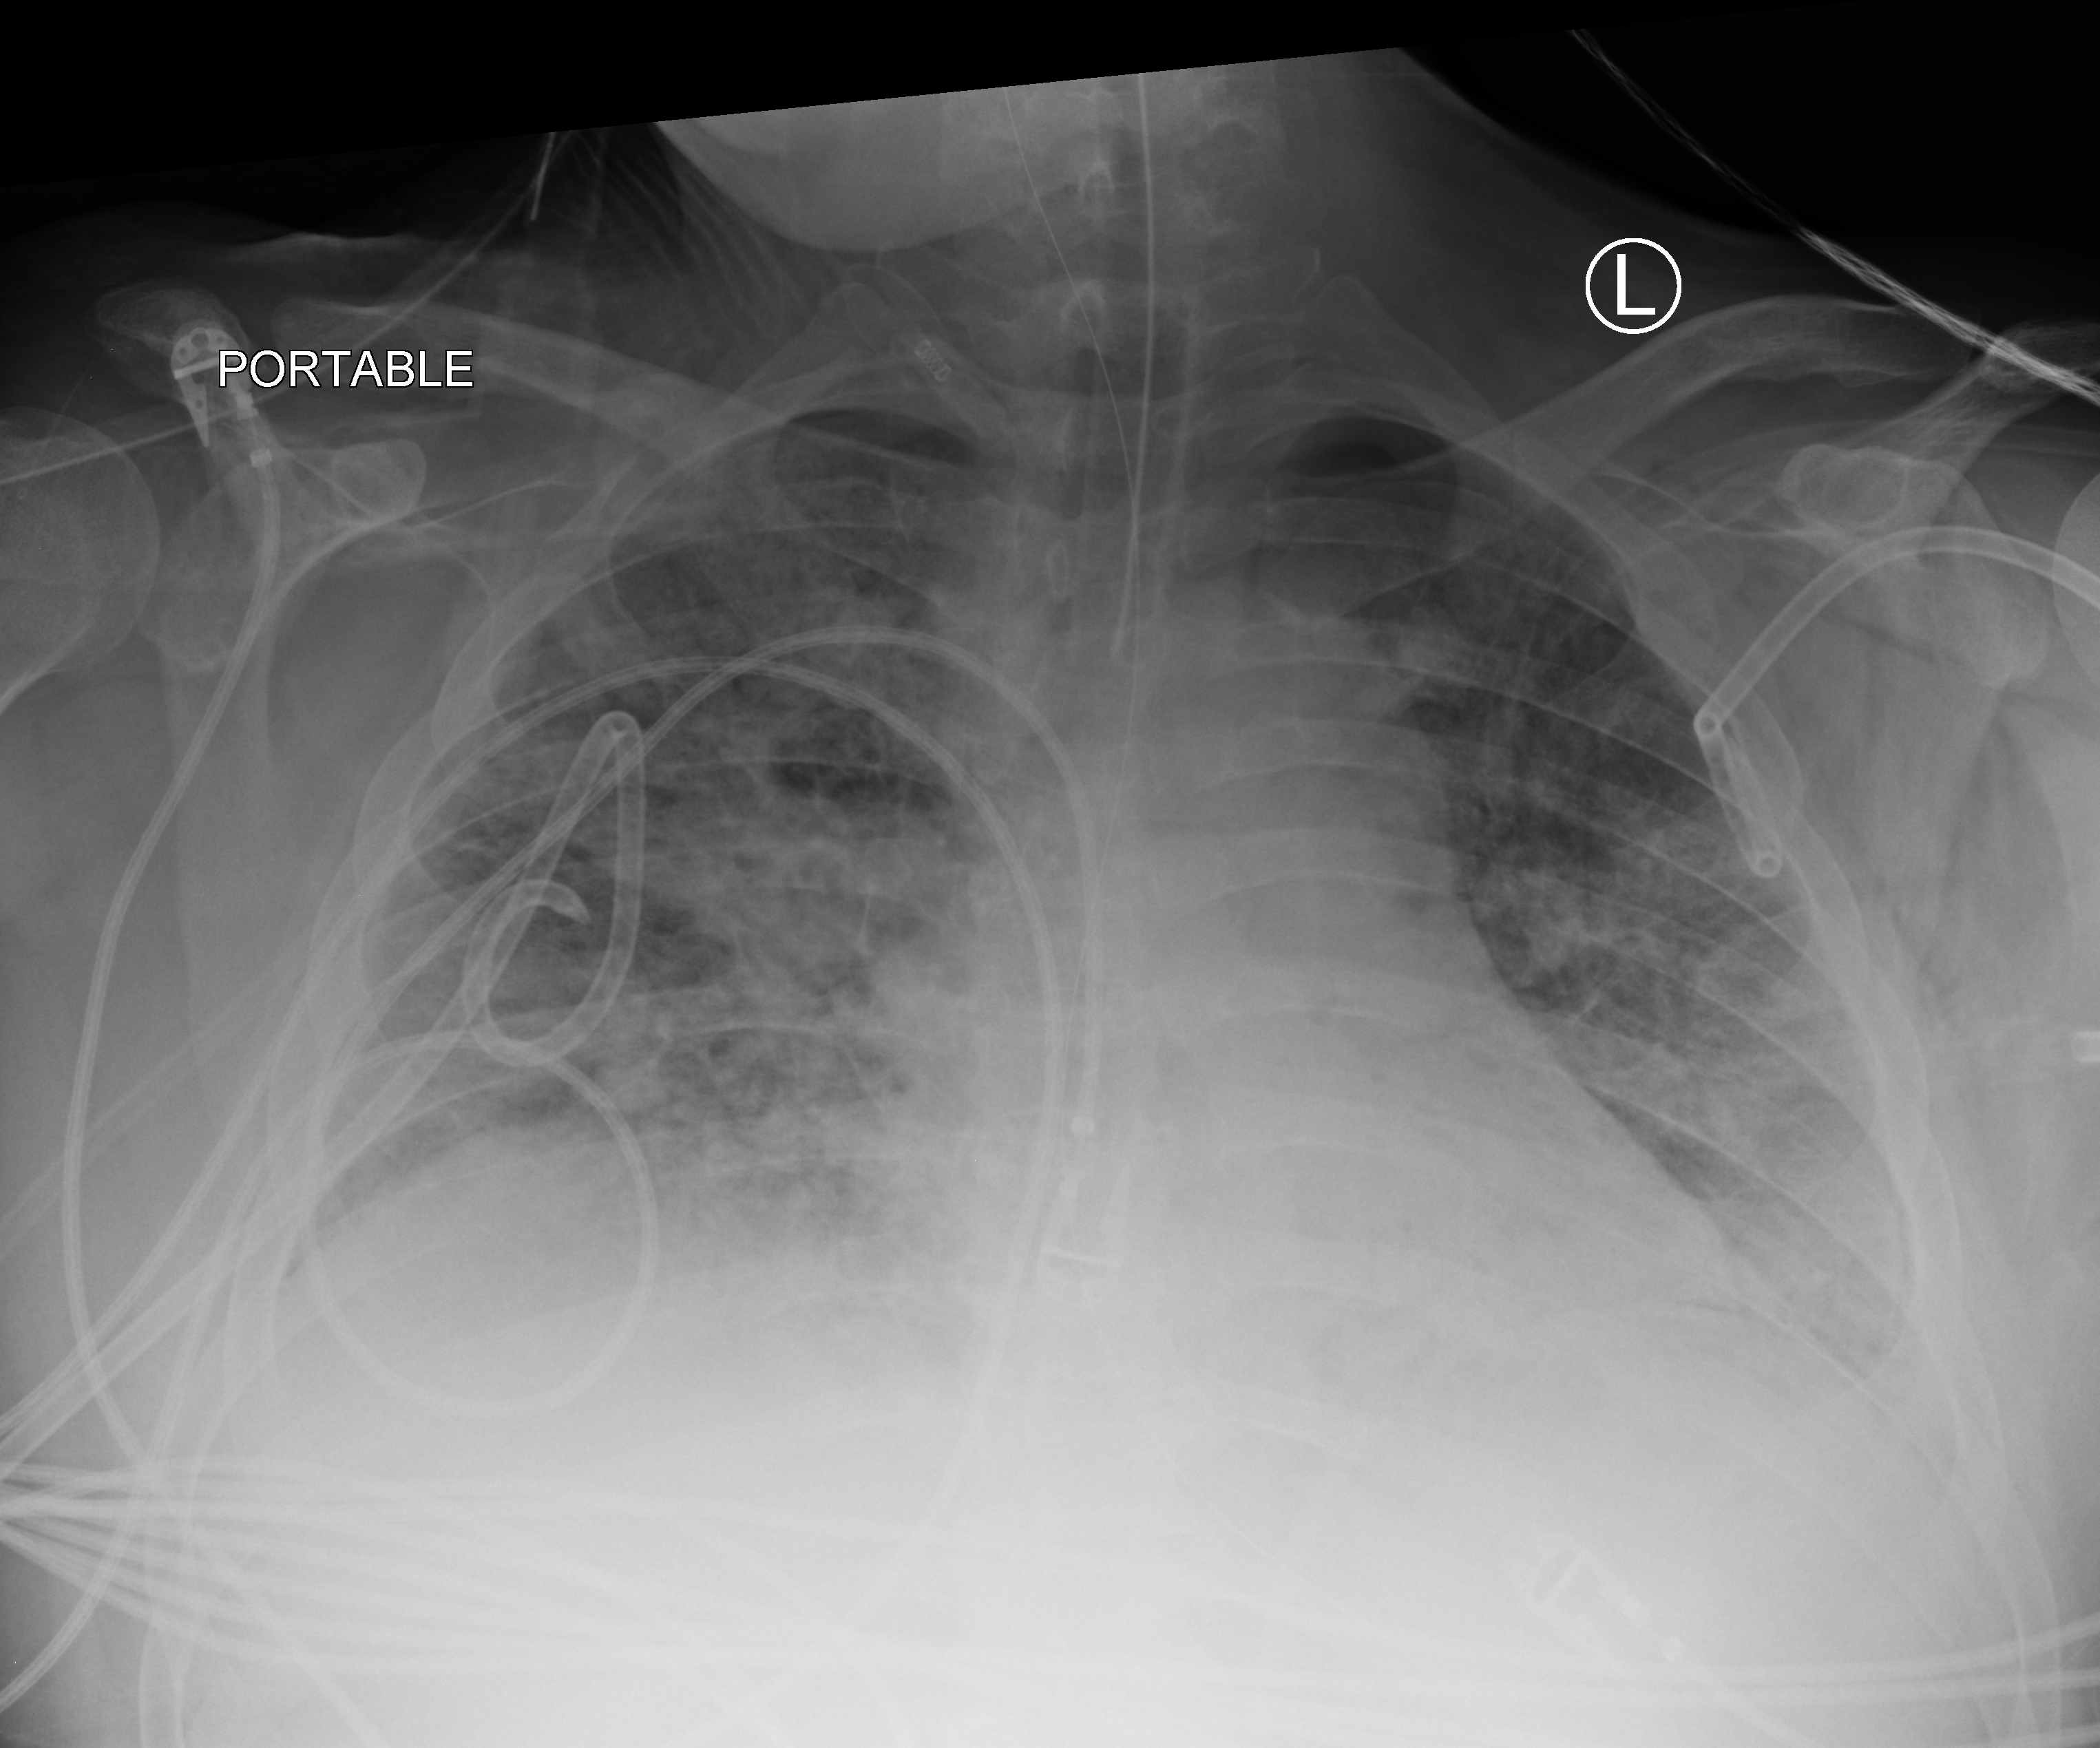
Chest X-ray (portable), anteroposterior (AP) projection. Adult patient hospitalised with COVID-19, age 18–59 years.
From the hospital-stay record, not from the radiograph (when in the stay this image was taken is not recorded):
- mechanically ventilated during this hospital stay: yes
- length of hospital stay: 31 days
- admitted to intensive care during this hospital stay: yes